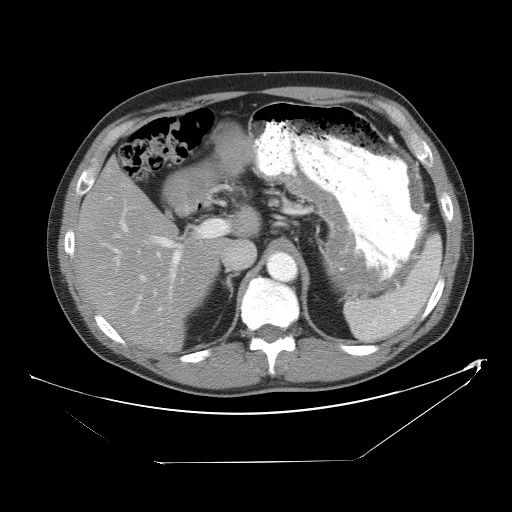
Contrast-enhanced abdominal CT, one axial slice; slice 34 of 53 in the series (ordered by position); 120 kVp; intravenous contrast given; soft-tissue window (W 400 / L 40 HU); 5 mm slice thickness; 512 × 512 image matrix. Male patient, age 59 years. Case-level facts recorded for this patient, not image findings: diagnosis: colorectal cancer liver metastases, imaged before liver resection; multiple liver metastases: yes; largest metastasis: 8.5 cm; disease in both lobes: no.
Structures marked on this image (outlined manually by an expert reader):
- hepatic veins: bounding box (x1, y1, x2, y2) in pixels: (114, 208, 161, 295)
- liver: (77, 144, 257, 353)
- planned liver remnant (the part of the liver to remain after resection): (78, 163, 222, 353)
- portal vein (with intrahepatic branches): (113, 220, 229, 301)